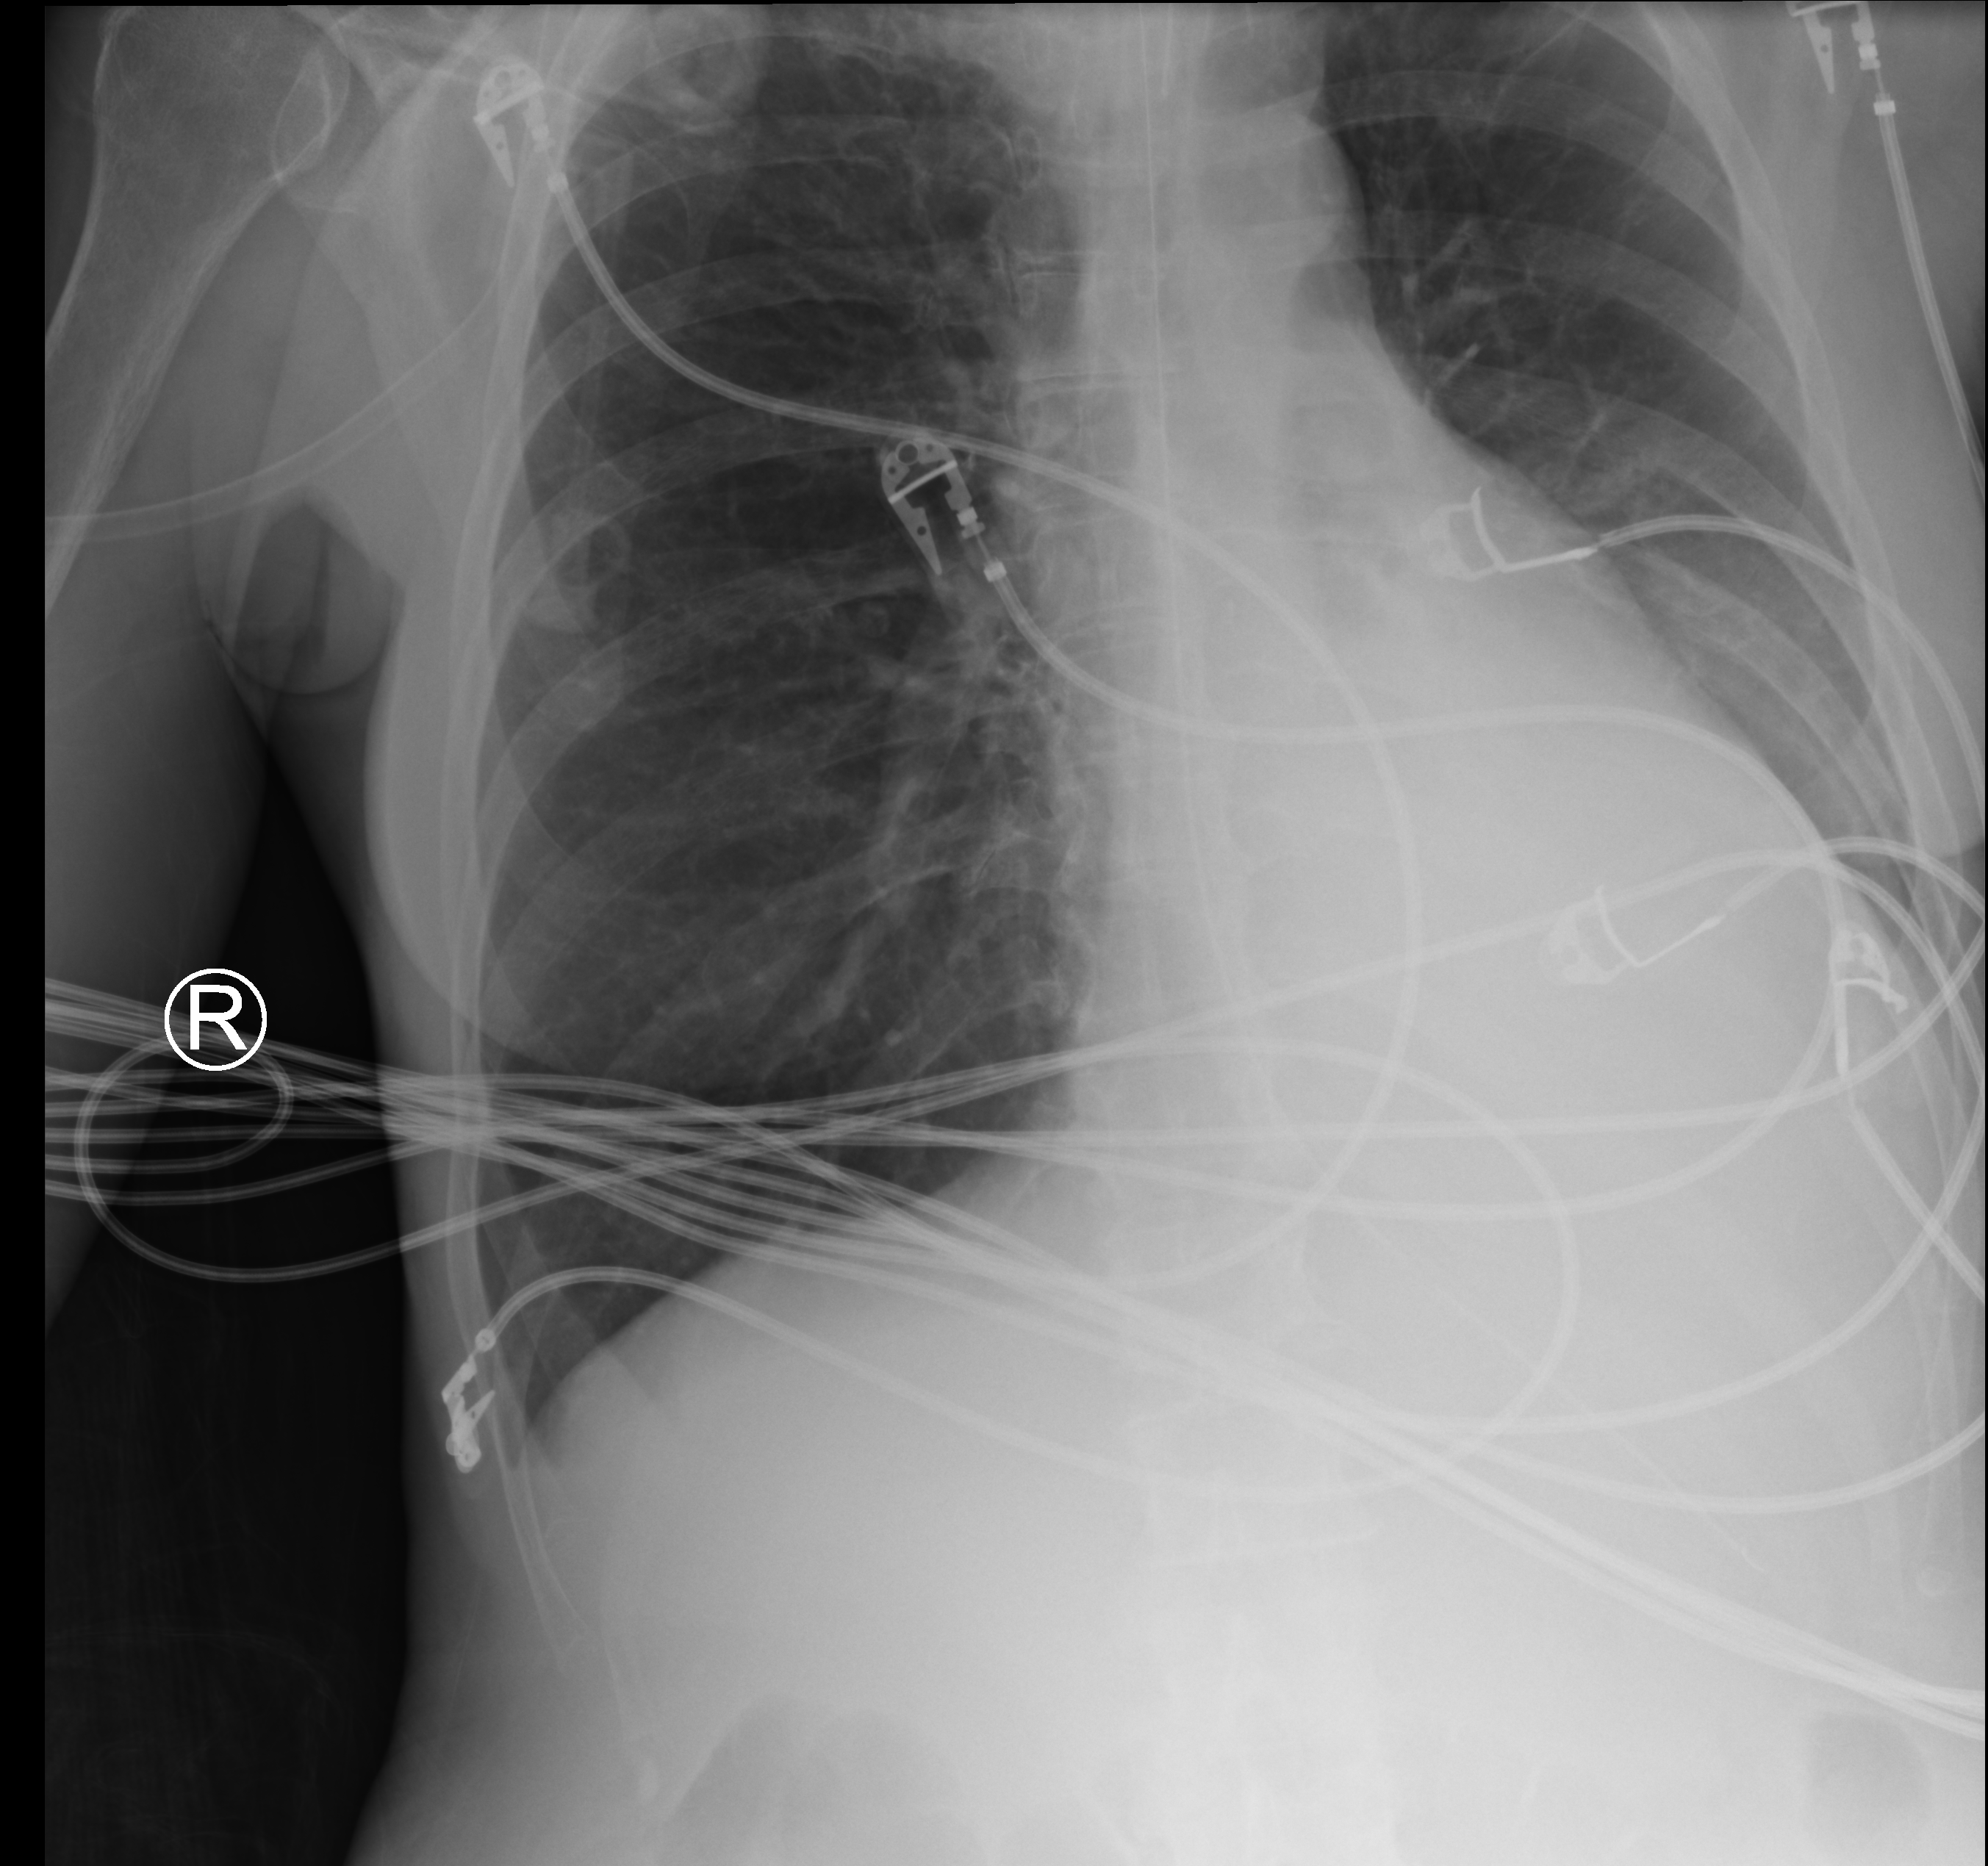
Chest X-ray (portable), anteroposterior (AP) projection. Female patient hospitalised with COVID-19, age 60–74 years.
Admission-level facts for this patient (not findings on this image; timing relative to this image not recorded): mechanically ventilated during this hospital stay: yes.